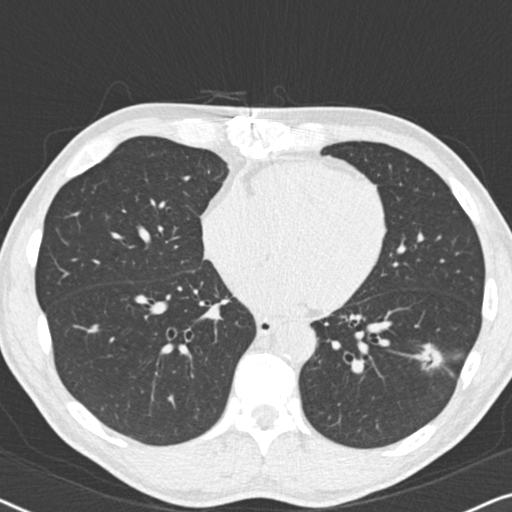
Low-dose screening chest CT, axial slice, second screening round (one year after baseline), lung window (W 1500 / L -600 HU), standard (soft-tissue) reconstruction kernel (B30f), 512 × 512 image matrix, field of view 330 × 330 mm. Male participant, aged 59 years at enrolment. Current smoker at enrolment.
• Expert-annotated lung lesion, bounding box [x1, y1, x2, y2] px = [411, 335, 463, 382].
• The screening reader recorded 2 non-calcified nodules or masses ≥4 mm on this exam (left lower lobe, right middle lobe); which of them this box marks is not recorded.
• Lung cancer was diagnosed 484 days after this screen (after the third annual screen): adenocarcinoma, NOS, left lower lobe, poorly differentiated (G3), stage IA (AJCC 6th edition), 20 mm at pathology.